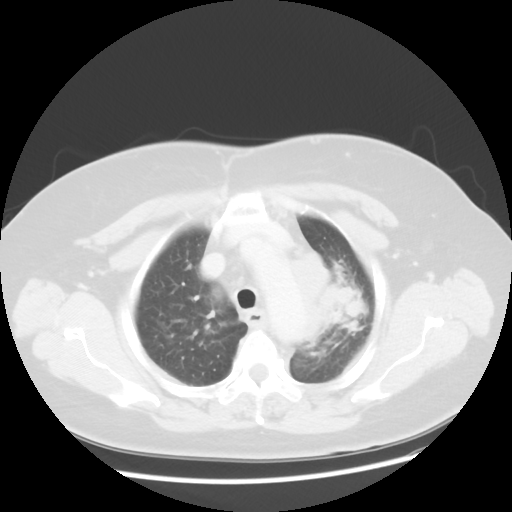
Chest CT, one axial slice. 120 kVp. Lung window (W 1500 / L -600 HU). 5 mm slice thickness. 512 × 512 image matrix, field of view 374 × 374 mm. Patient: female, 58 years. Case-level facts recorded for this patient, not image findings: clinical TNM (as recorded): T4 N3 M0; histopathological grade: G3.
Outlined on this slice (rectangle marked by the reading radiologist):
- lung tumour (recorded histology: small cell carcinoma): box from (x=291, y=242) to (x=370, y=345) px